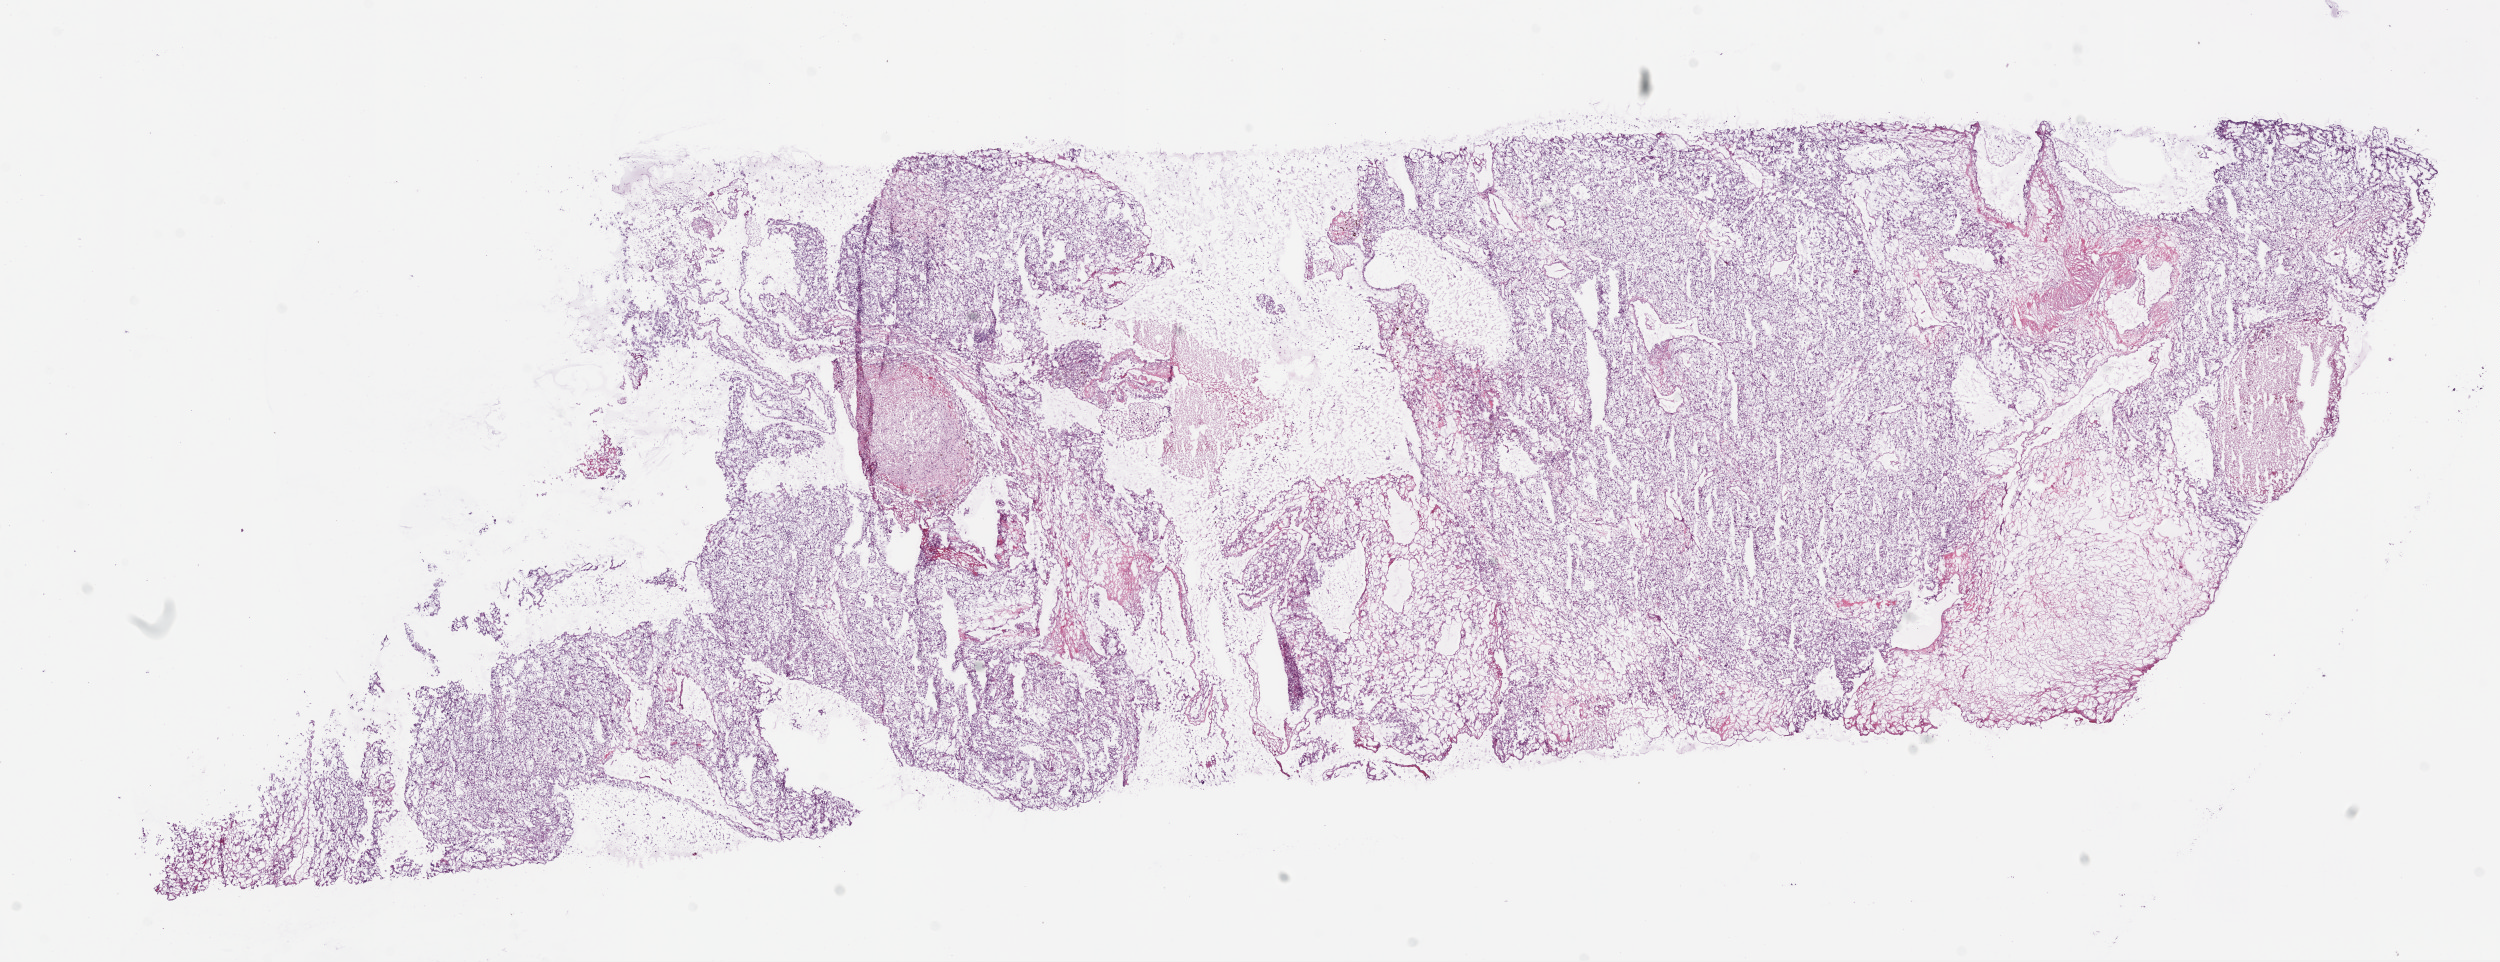
H&E-stained whole-slide image, shown as a low-resolution overview of the whole scanned area (about 20.1 x 7.7 mm, from a 20x scan), frozen section from the bottom of the tissue portion, kidney, primary tumour sample. Male, age 64 years at initial diagnosis. Histologic grade: G4 (undifferentiated). Pathologist review of this section (percent, as recorded): tumour cells 90%, tumour nuclei 85%, normal cells 0%, stromal cells 10%, necrosis 0%.
Lymph nodes positive (case pathology): 0 of 1 examined. Diagnosis: Clear cell adenocarcinoma, NOS. AJCC pathologic stage: IV.